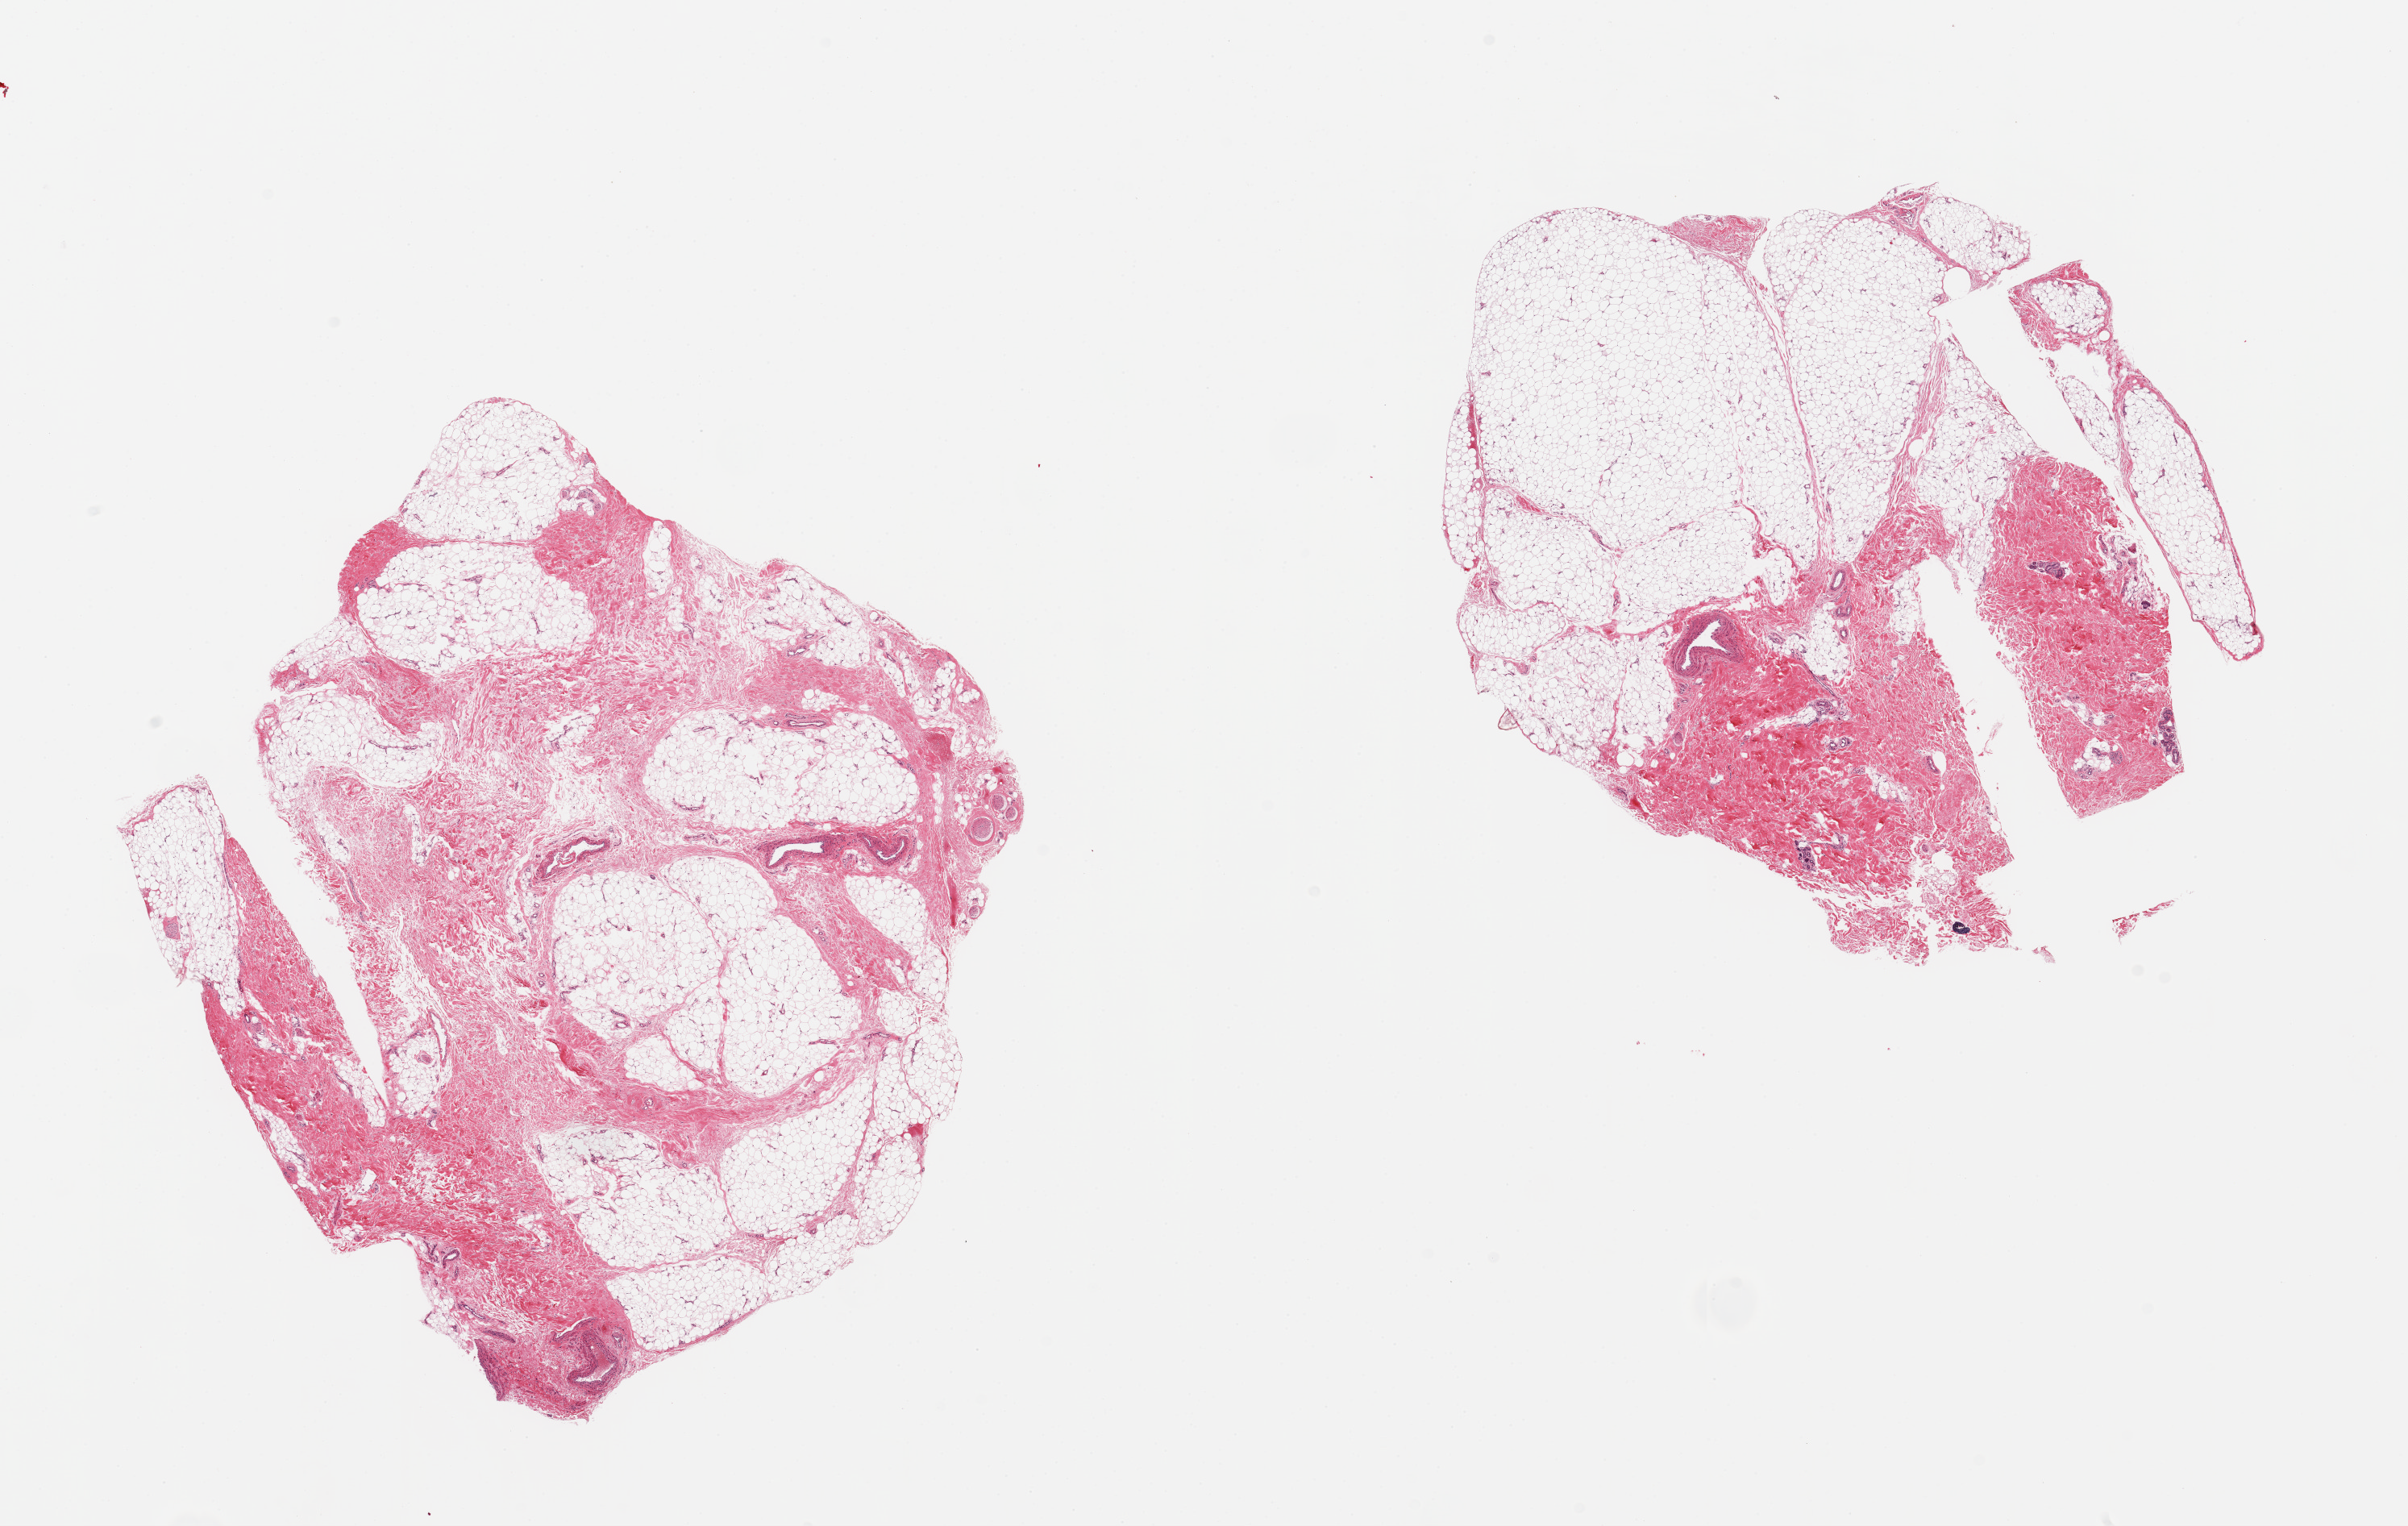
Whole-slide image, H&E stain — whole scanned area (about 23.6 x 15.0 mm) shown as a low-resolution overview. PAXgene-fixed paraffin-embedded (PFPE) section. Section of adipose tissue (target tissue). Tissue donor sample. Donor: male.
* review note (as recorded): 2 pieces, ~50% fascia